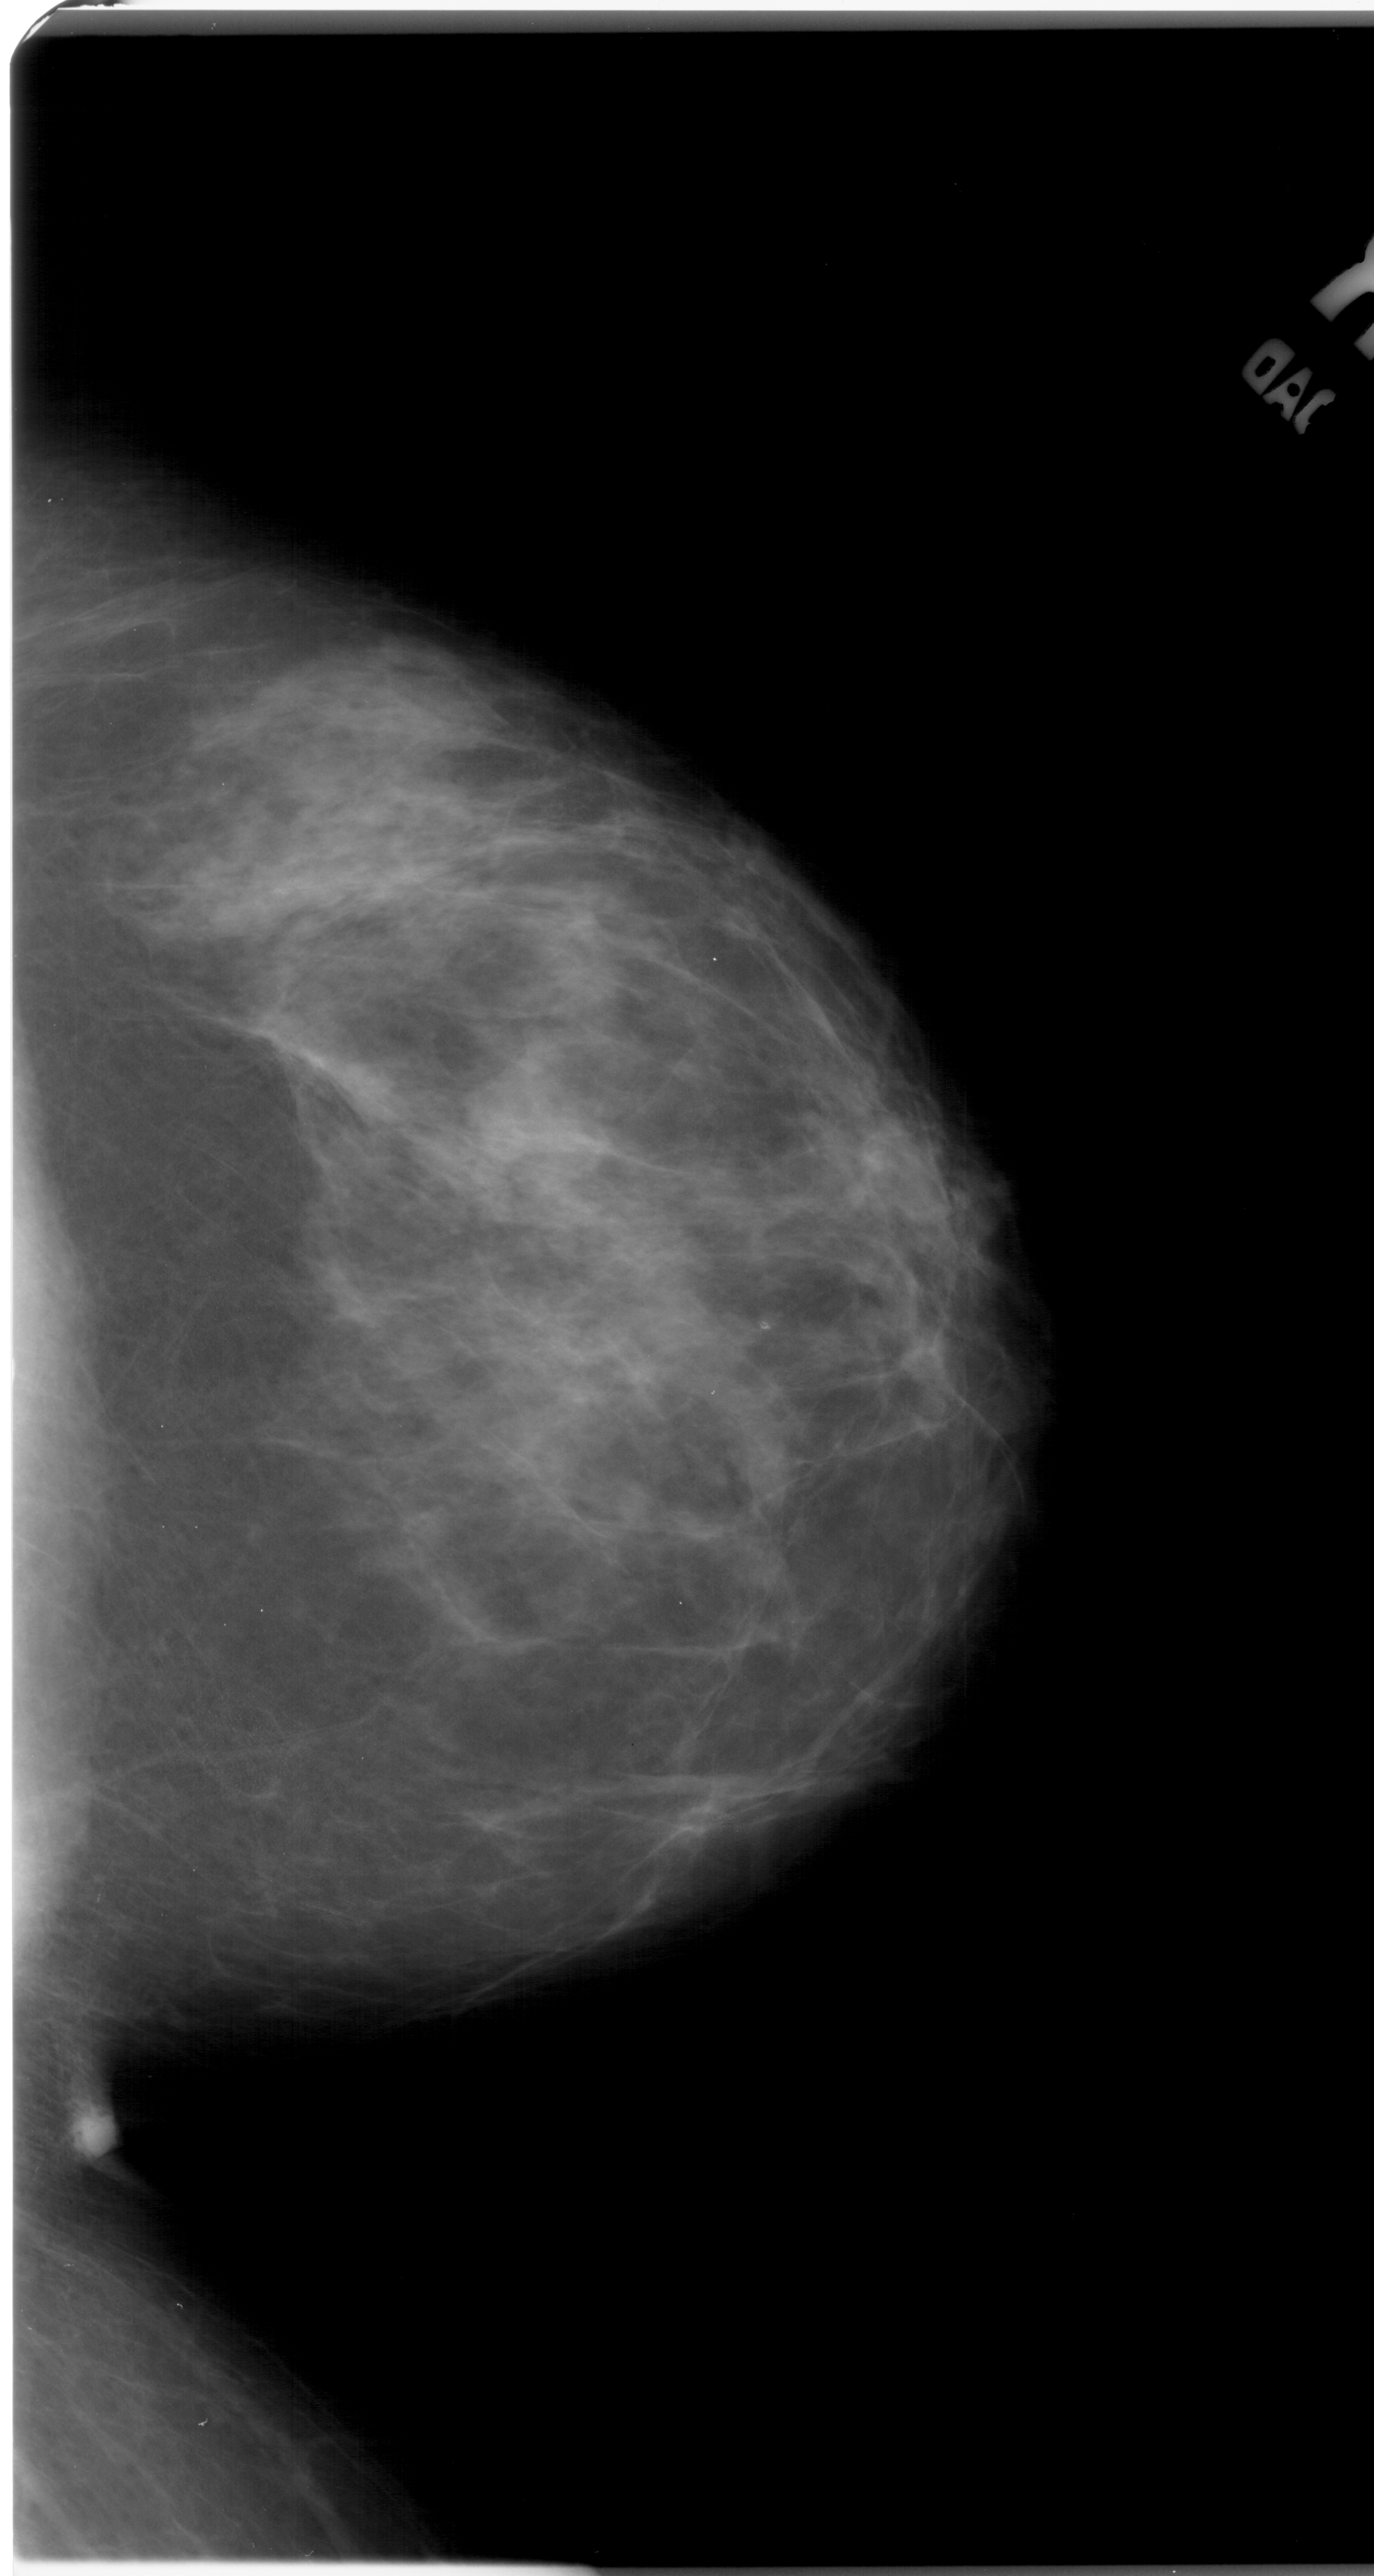
Digitized screen-film mammogram; right breast; craniocaudal (CC) view; breast composition: heterogeneously dense (BI-RADS density category 3 of 4); 1374 × 2576 image matrix.
Marked abnormalities (boxes around the expert regions of interest):
- mass, shape lobulated, margins ill defined; BI-RADS assessment category 4; subtlety rating 2 on a 1 (subtle) to 5 (obvious) scale; pathology result (as recorded, not read from the image): benign: bounding box (x1, y1, x2, y2) in pixels: (479, 1073, 601, 1164)